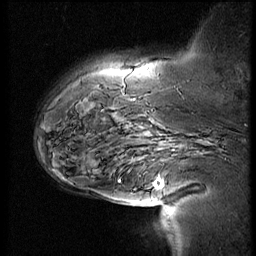
Breast MRI (dynamic contrast-enhanced), one sagittal slice; slice 16 of 60 in the series (ordered by position); 4 images stored at this slice position (order not interpretable as contrast timing); 1.5 T; TE 4.2 ms, TR 9 ms; 256 × 256 image matrix. Female patient, age 56 years. From the clinical record (not read from this slice): setting: breast cancer imaged before/during neoadjuvant chemotherapy; receptor status: HER2-positive.
Annotated regions visible in this slice (semi-automatic segmentation, software-assisted and operator-edited):
- analysis volume of interest (the breast-tissue region the enhancement analysis was run in; not a lesion): bounding box (x1, y1, x2, y2) in pixels: (110, 138, 192, 201)
- tumour enhancement mask (voxels above the 140 % enhancement threshold inside the analysis volume of interest): (119, 178, 162, 187)